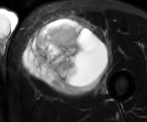
MRI of an extremity soft-tissue mass, one axial slice. Position 38 of 52 along the scan axis. T2-weighted fat-saturated. MR volume resampled by the dataset authors to the PET/CT grid (not the native acquisition matrix). 3.27 mm slice thickness. 147 × 122 image matrix, field of view 144 × 119 mm. Male patient. From the clinical record (not read from this slice): histological type: pleiomorphic liposarcoma; grade: high; site of the primary tumour: left thigh.
Structures marked on this image (expert contour drawn on MRI and transferred to this co-registered scan by the dataset authors):
- gross tumour volume including surrounding oedema: box from (x=25, y=16) to (x=111, y=93) px
- gross tumour volume (mass): (x=25, y=18)–(x=108, y=93)